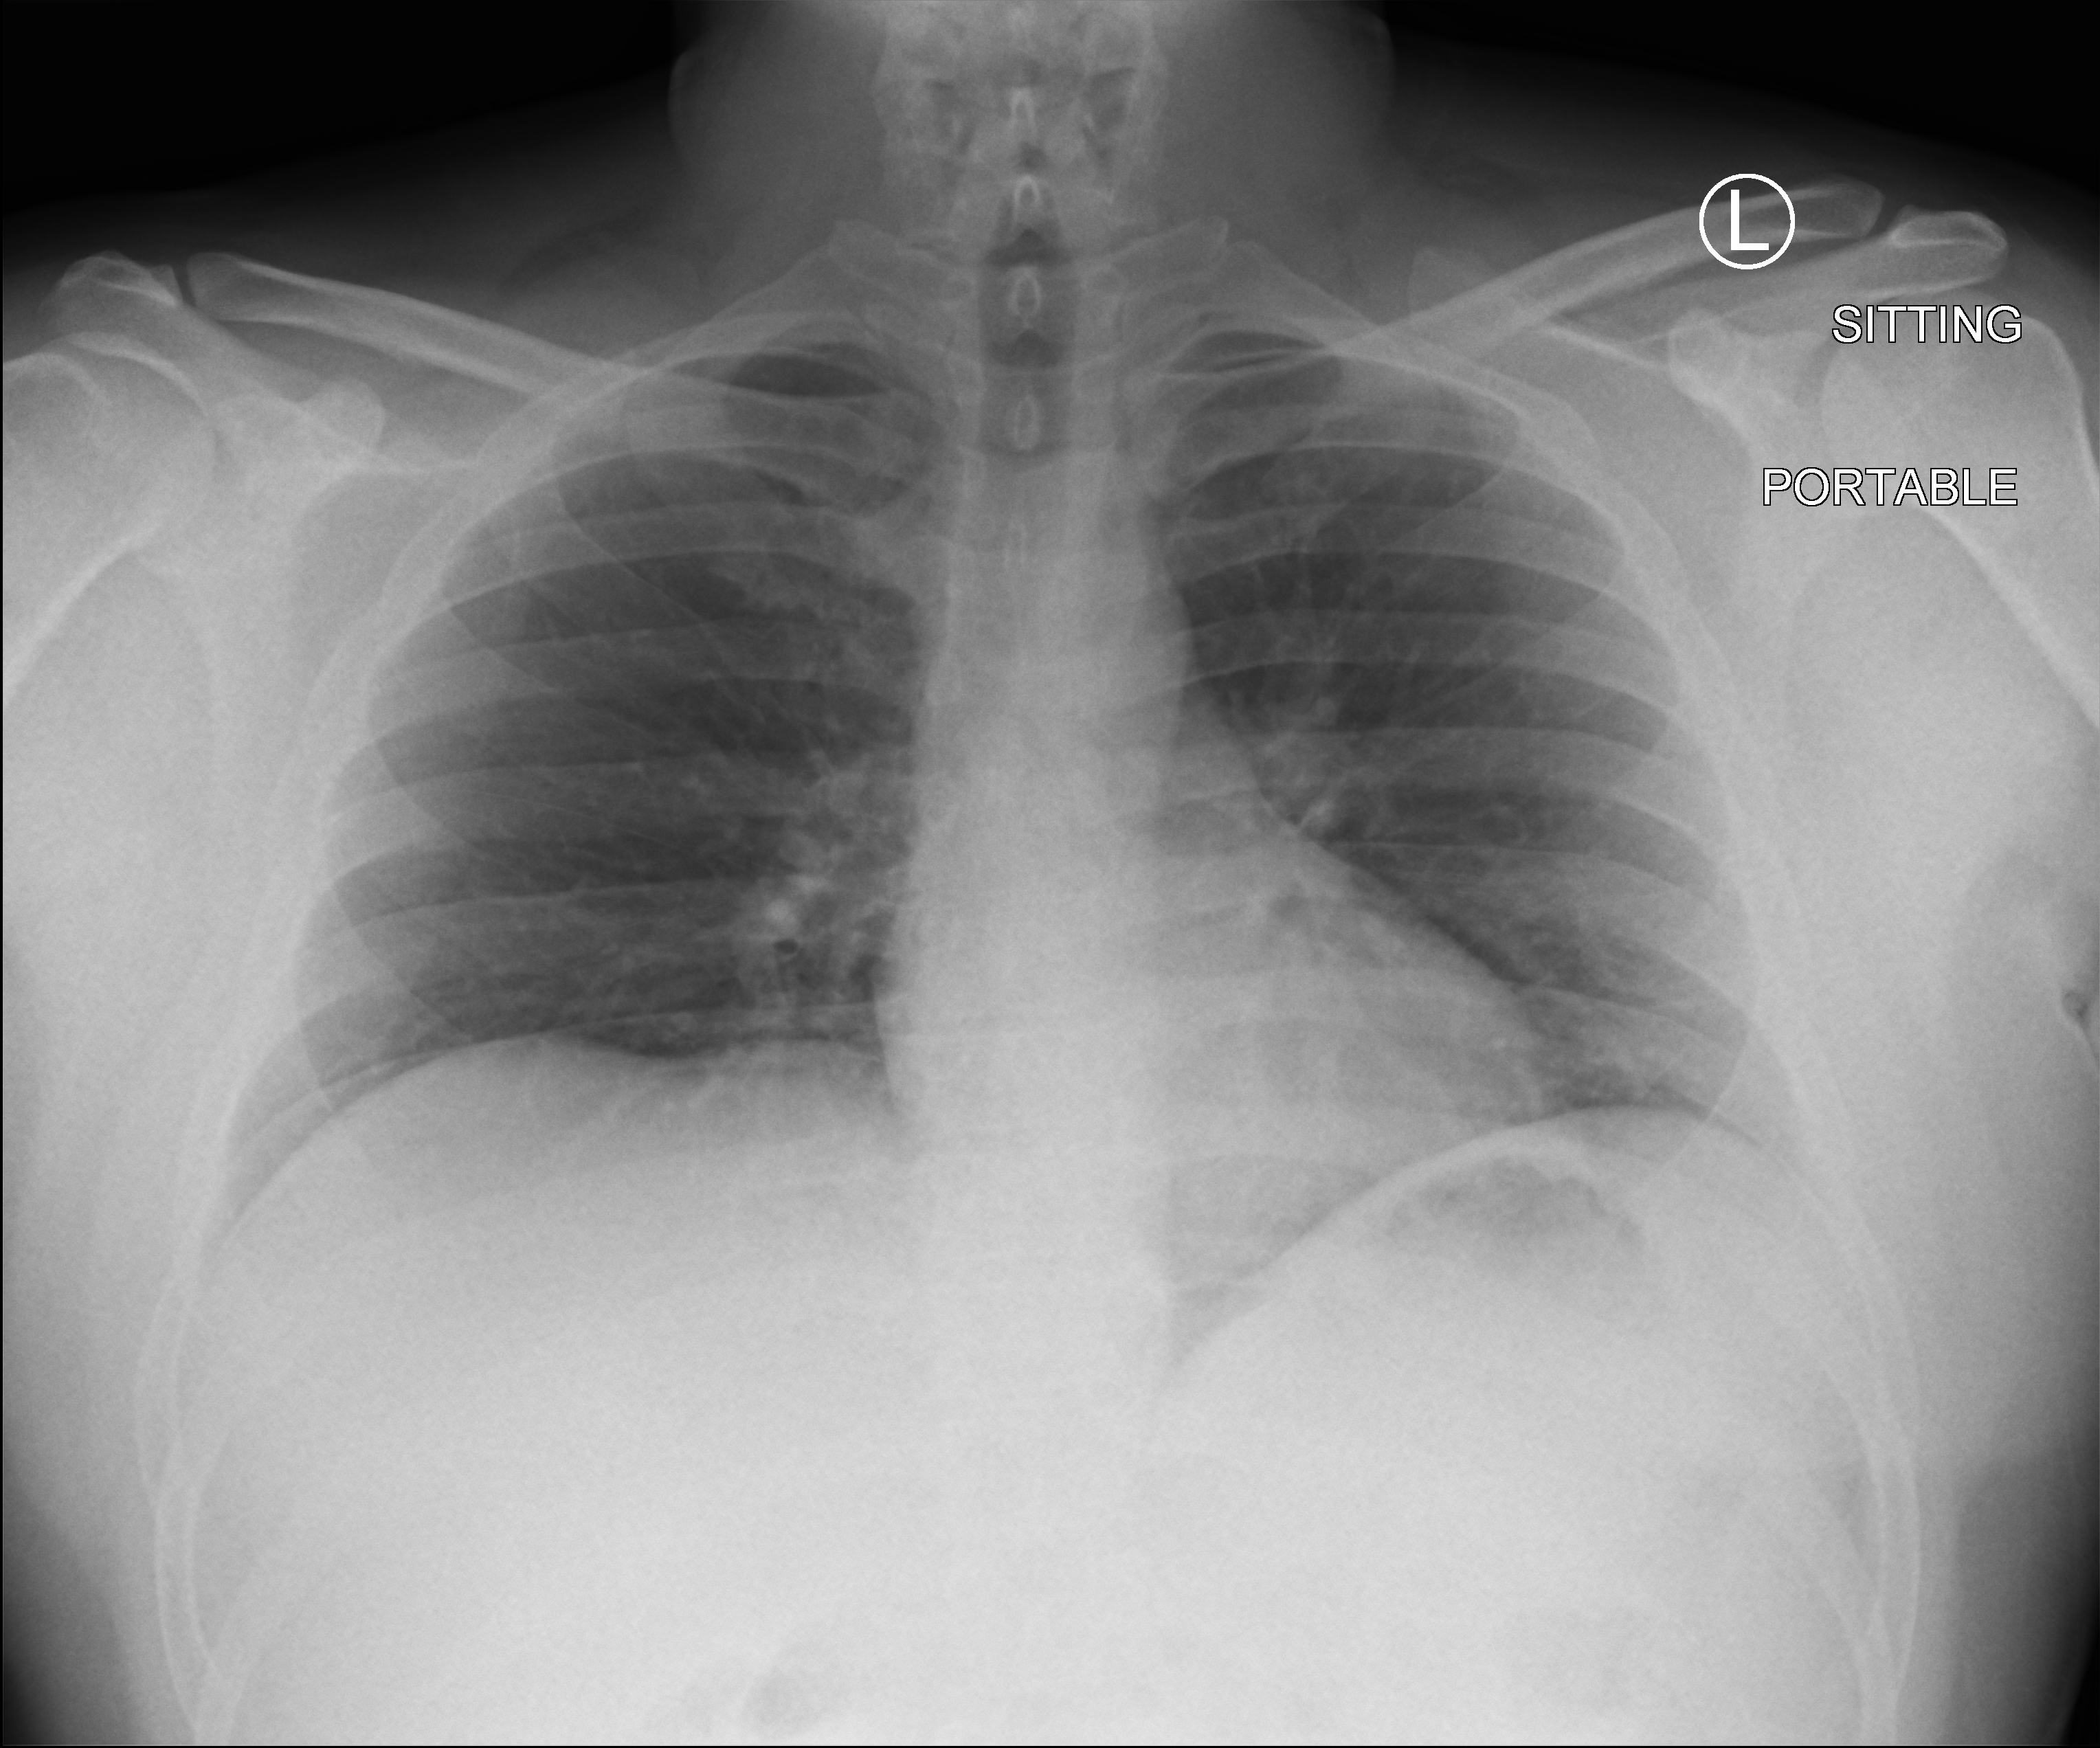
Chest X-ray (portable), anteroposterior (AP) projection. Patient hospitalised with COVID-19; male, aged 18–59 years.
Admission-level facts for this patient (not findings on this image; timing relative to this image not recorded): admitted to intensive care during this hospital stay: no; mechanically ventilated during this hospital stay: no; hypertension (admission record): no.